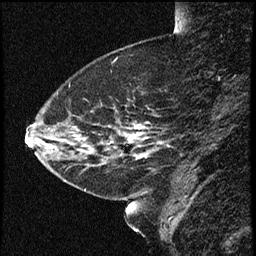
Breast MRI (dynamic contrast-enhanced), one sagittal slice. Position 15 of 60 along the scan axis. Dynamic contrast-enhanced study with each time point stored as its own series, time point 2 of 4 at this slice position (early post-contrast, ordered by acquisition time). 1.5 T. TE 4.2 ms, TR 16.7 ms. 2 mm slice thickness. 256 × 256 image matrix, field of view 200 × 200 mm. Female patient, age 52 years. From the clinical record (not read from this slice): setting: breast cancer imaged before/during neoadjuvant chemotherapy; receptor status: HER2-positive.
Structures marked on this image (semi-automatically segmented with operator editing):
- analysis volume of interest (the breast-tissue region the enhancement analysis was run in; not a lesion): box from (x=37, y=79) to (x=163, y=181) px
- tumour enhancement mask (voxels above the 100 % enhancement threshold inside the analysis volume of interest): (x=131, y=128)–(x=137, y=138)